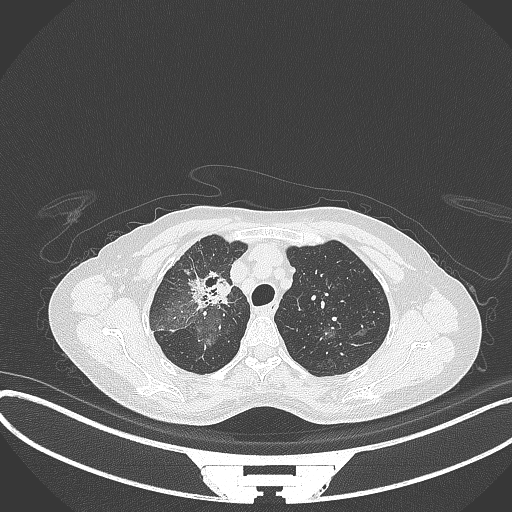
Chest CT, one axial slice. Slice 249 of 284 in the series (ordered by position). Reconstruction kernel B70f. 120 kVp. Lung window (W 1500 / L -600 HU). 1 mm slice thickness. 512 × 512 image matrix. Patient: female, 59 years. Case-level facts recorded for this patient, not image findings: clinical TNM (as recorded): T3 N0 M0.
Outlined on this slice (bounding box drawn by a radiologist):
- lung tumour (recorded histology: adenocarcinoma): bounding box [x1, y1, x2, y2] px = [189, 270, 235, 309]